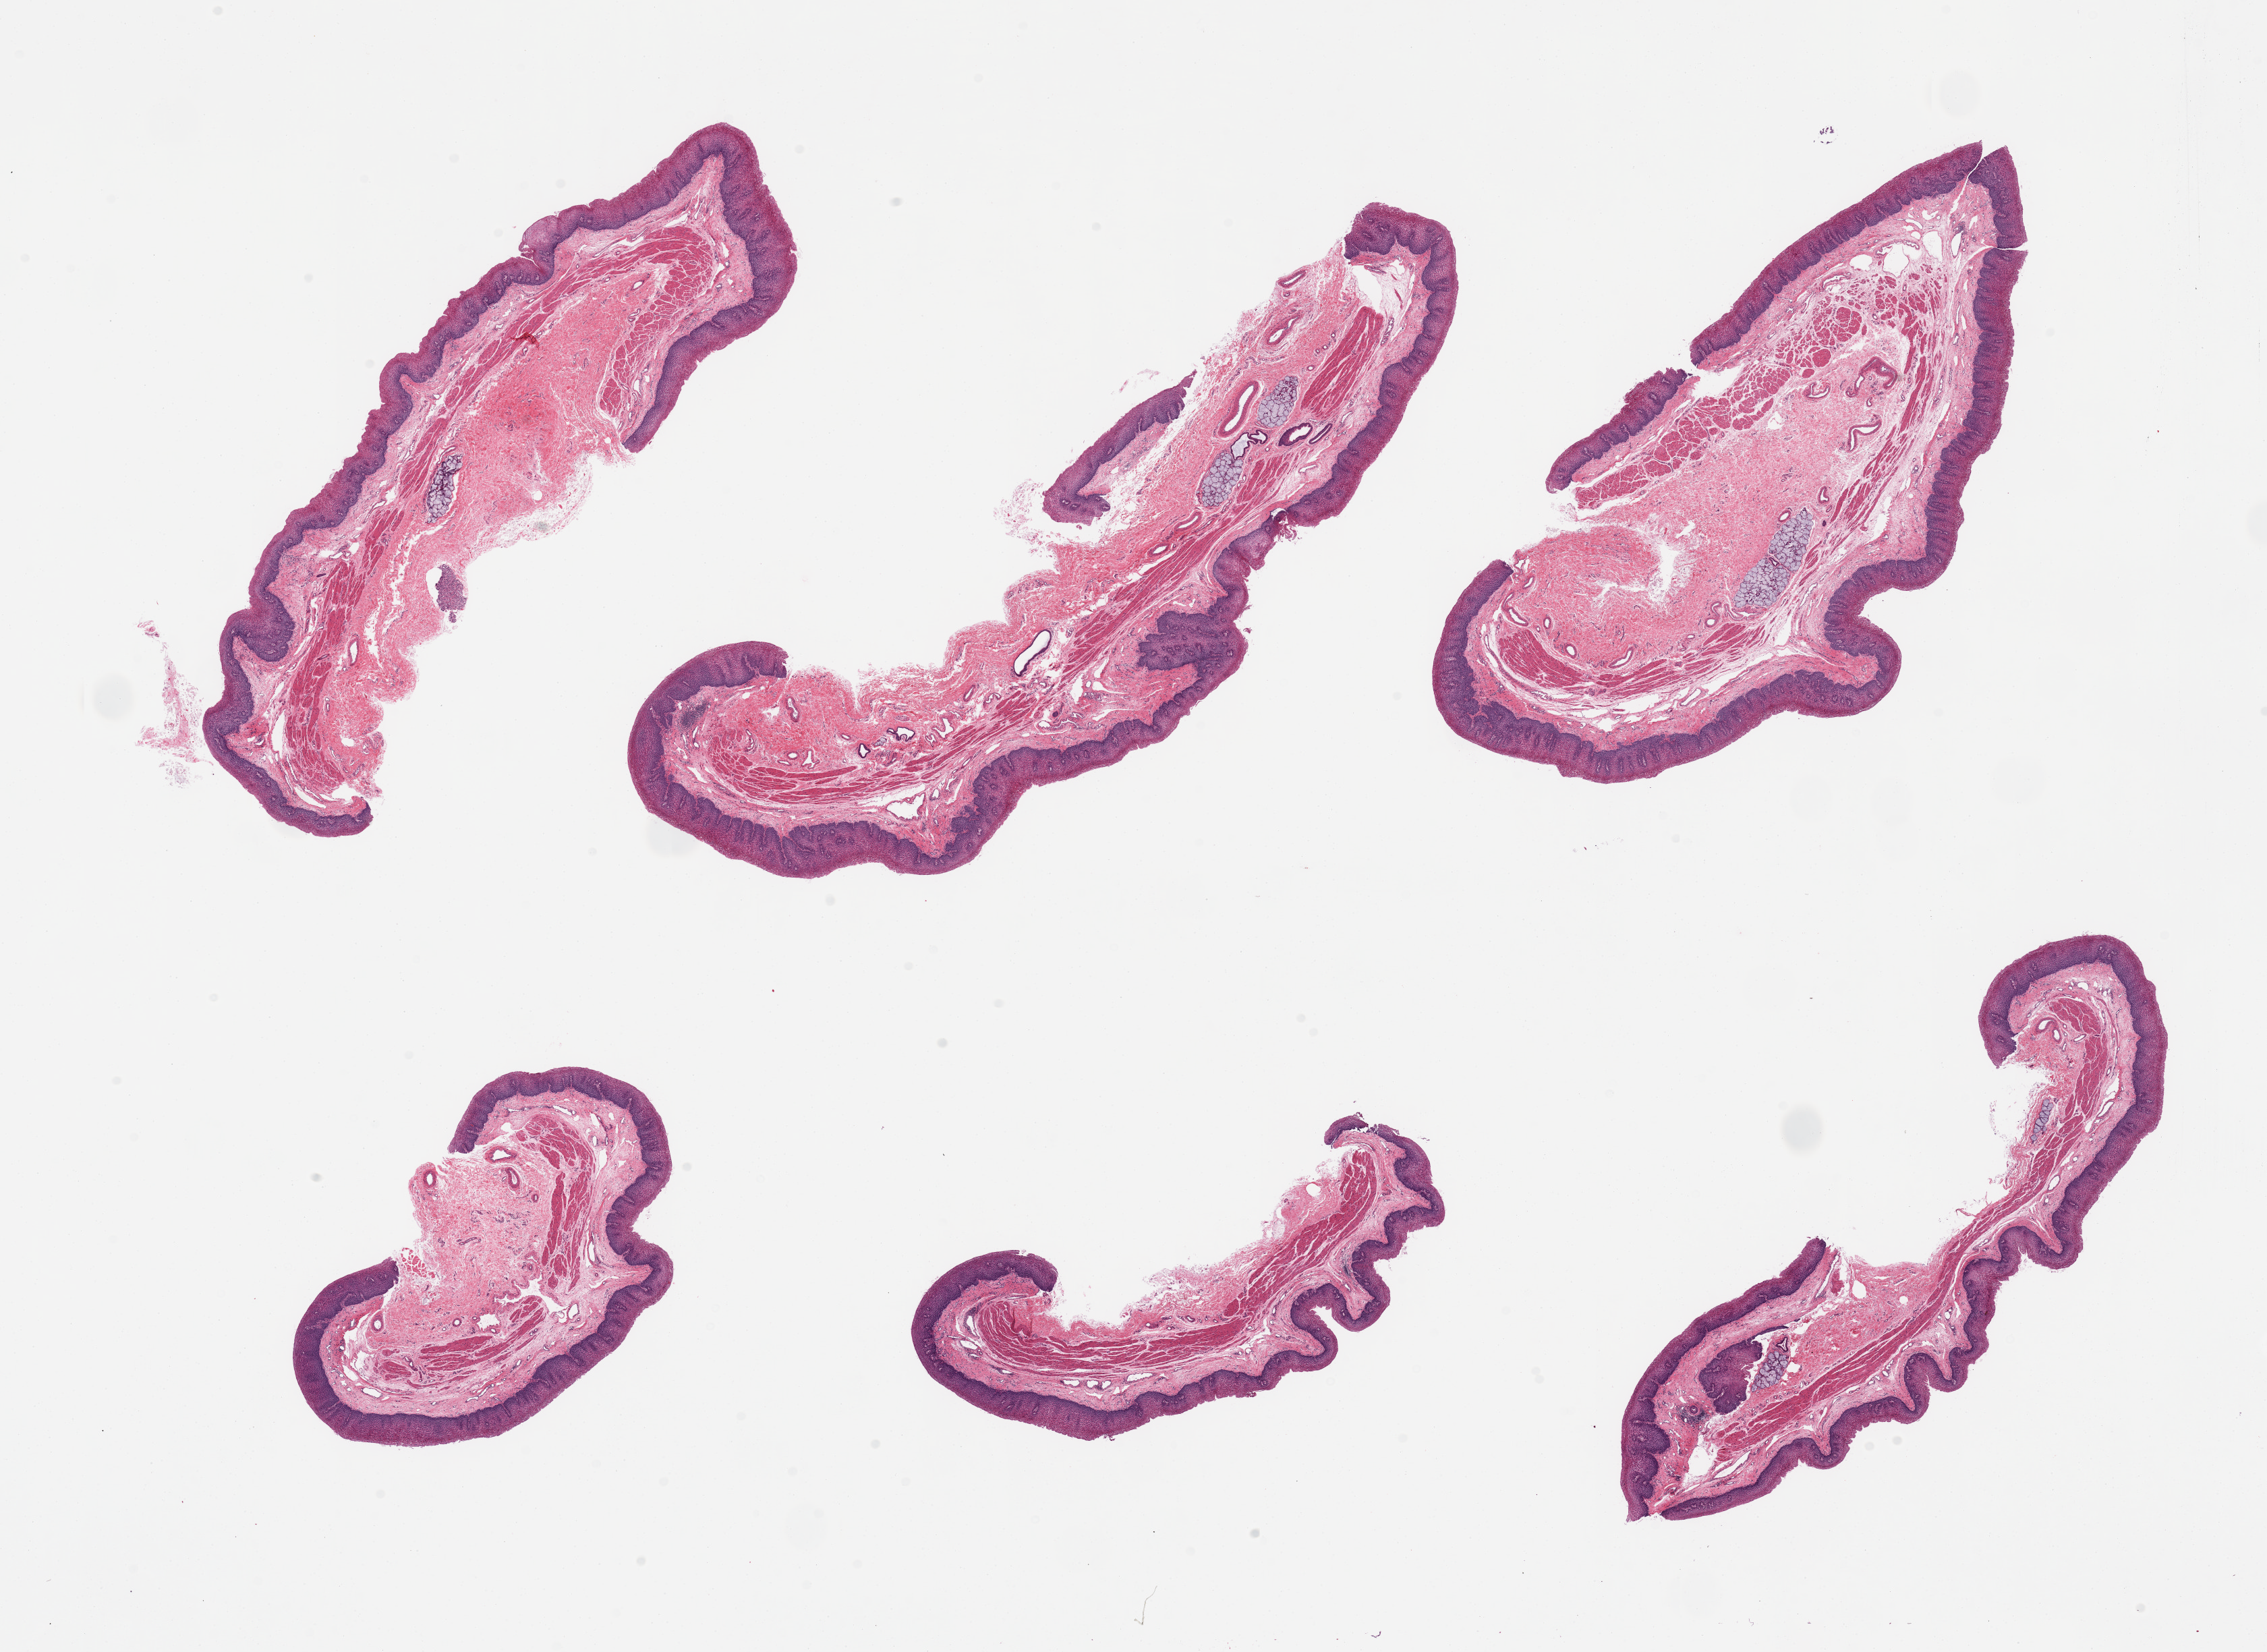
Haematoxylin and eosin whole-slide image, brightfield — whole scanned area (about 26.6 x 19.4 mm, acquisition: 20x scan) shown as a low-resolution overview. PAXgene-fixed, paraffin-embedded tissue. Section of esophageal mucous membrane (target tissue). Donor tissue sample. Male donor.
Review note (as recorded): 6 pieces, few groups of submucosal glands, detached fragment of adrenal tissue.